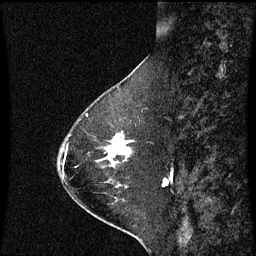
Breast MRI (dynamic contrast-enhanced), one sagittal slice; slice 20 of 60 in the series (ordered by position); dynamic contrast-enhanced series, image 2 of 3 at this slice position (ordered by acquisition); 1.5 T; TE 4.2 ms, TR 8.9 ms; 2 mm slice thickness; 256 × 256 image matrix, field of view 200 × 200 mm. Patient: female, 63 years. From the clinical record (not read from this slice): setting: breast cancer imaged before/during neoadjuvant chemotherapy; receptor status: HR-positive, HER2-negative.
Annotated regions visible in this slice (semi-automatic segmentation, software-assisted and operator-edited):
- analysis volume of interest (the breast-tissue region the enhancement analysis was run in; not a lesion): bounding box [x1, y1, x2, y2] px = [97, 132, 130, 167]
- tumour enhancement mask (voxels above the 70 % enhancement threshold inside the analysis volume of interest): [109, 134, 130, 165]